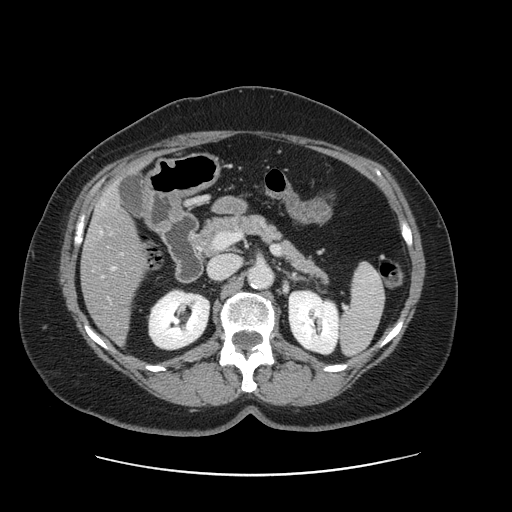
Contrast-enhanced abdominal CT, one axial slice; position 69 of 161 along the scan axis; intravenous contrast given; soft-tissue window (W 400 / L 40 HU); 512 × 512 image matrix. Female patient, age 62 years. From the clinical record (not read from this slice): diagnosis: colorectal cancer liver metastases, imaged before liver resection; multiple liver metastases: no; largest metastasis: 2.5 cm; disease in both lobes: no.
Structures marked on this image (expert manual segmentation):
- hepatic veins: bounding box <101,232,104,277> (left, top, right, bottom; pixels)
- liver: <82,188,145,343>
- portal vein (with intrahepatic branches): <113,267,115,269>